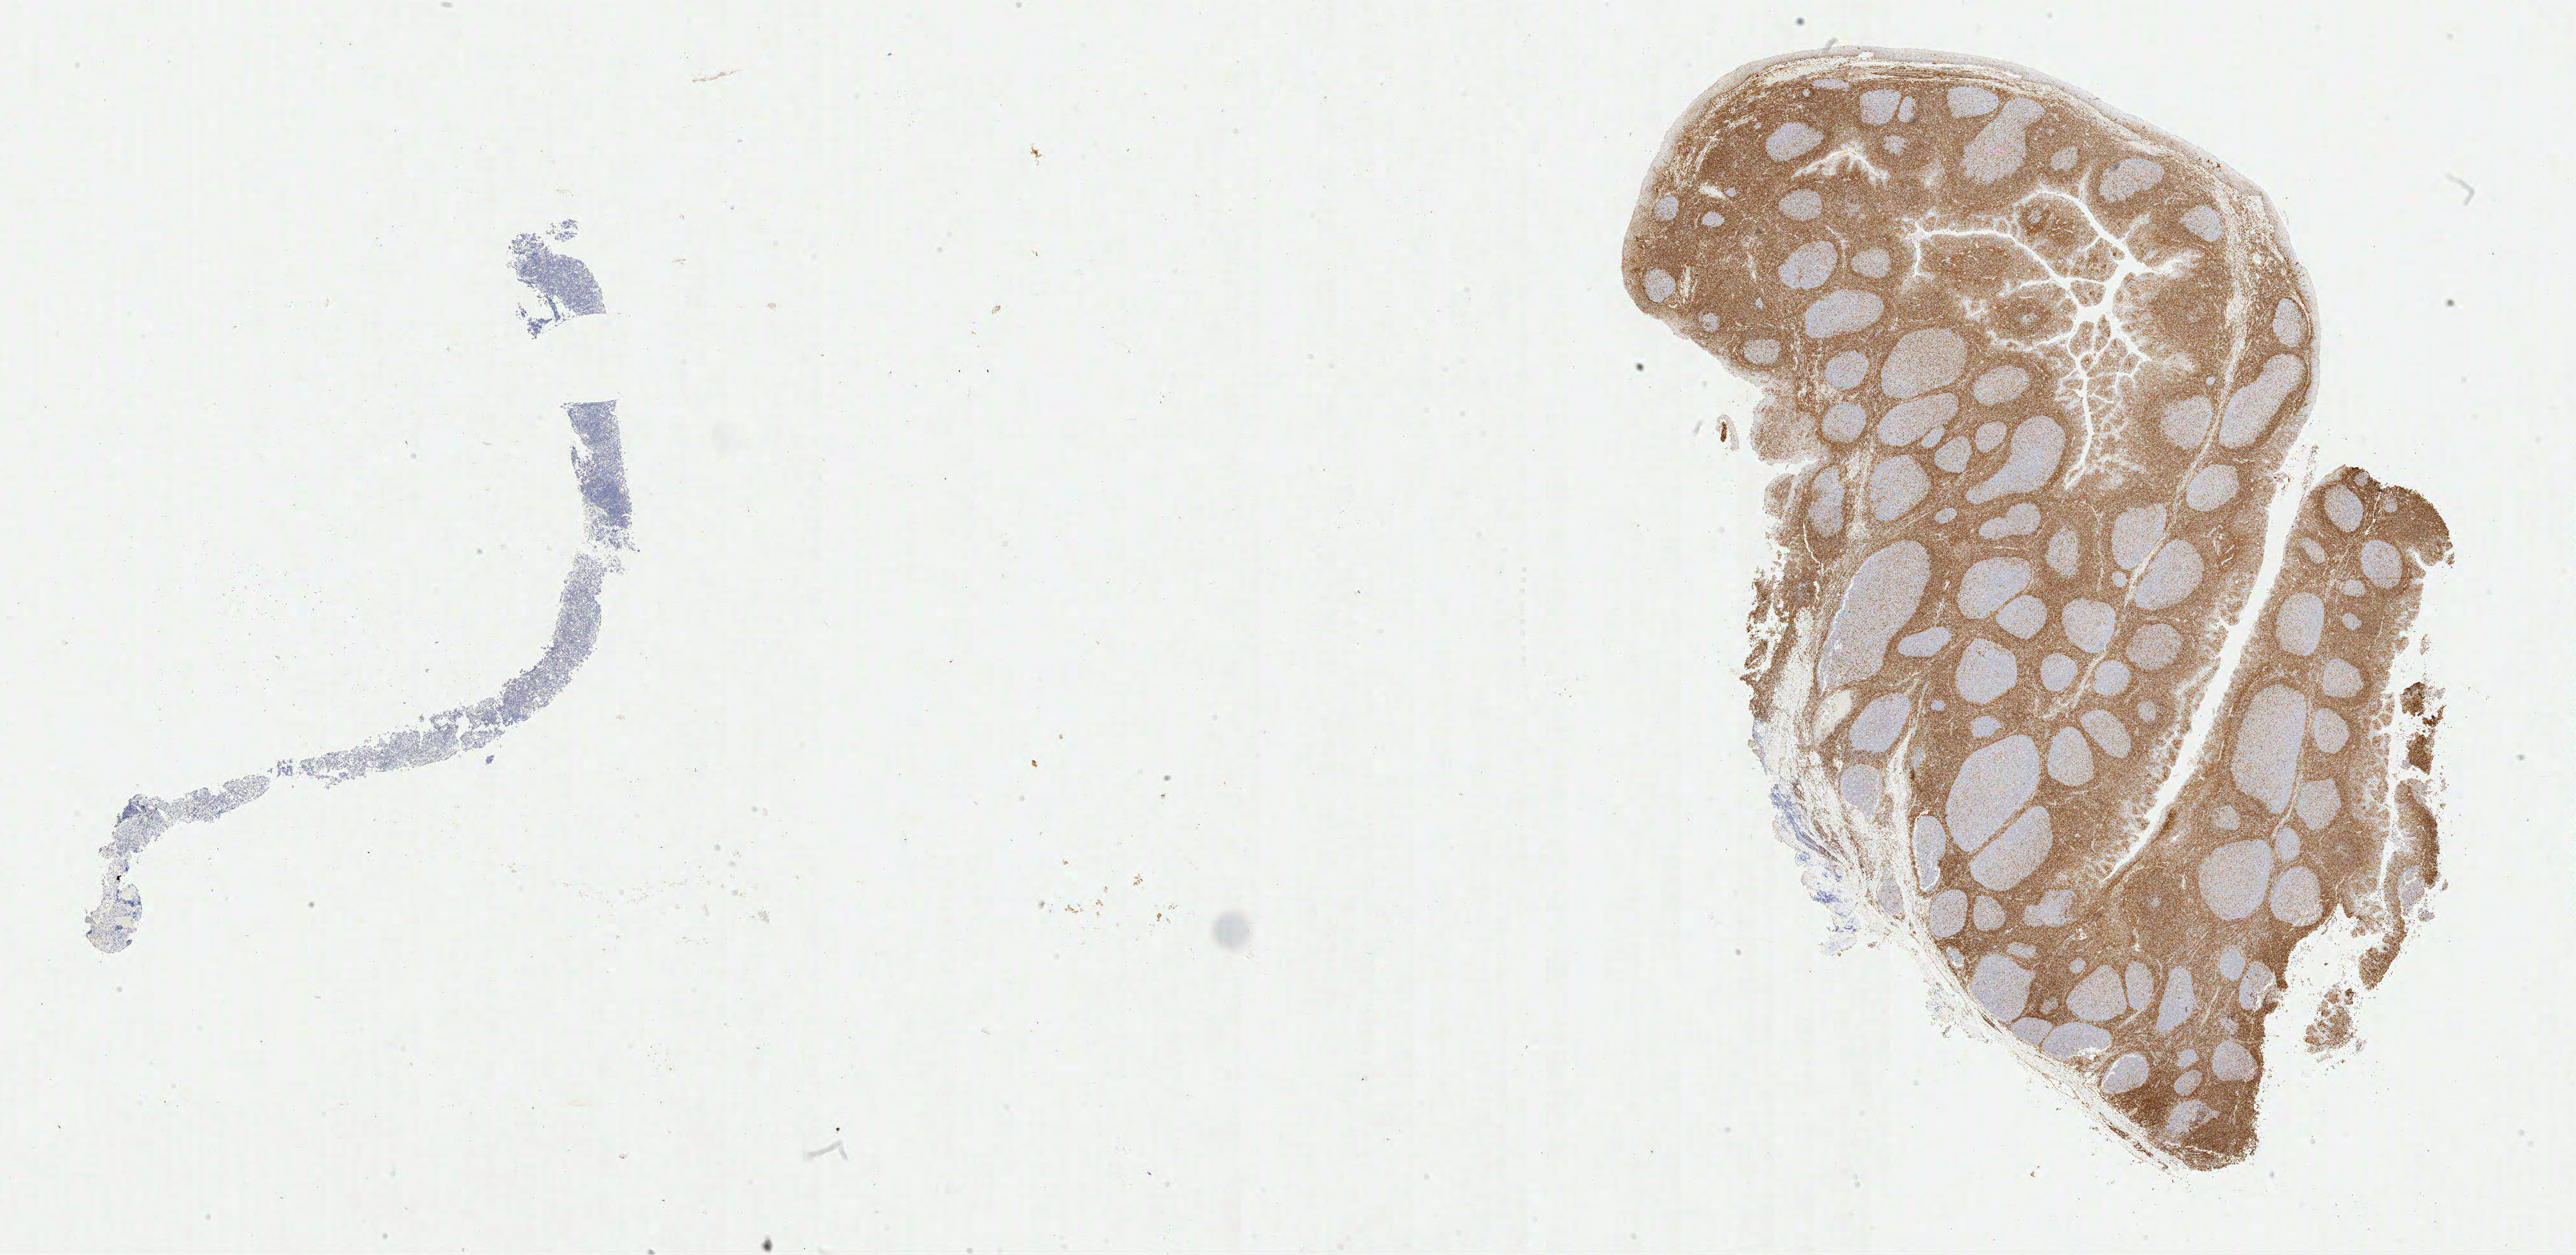
Whole-slide image, immunohistochemical stain for BCL2 — a low-resolution overview of the entire scanned area, about 31.7 x 15.4 mm, tumor tissue, anatomic site: ovary. Patient: female, age at initial diagnosis 7 years.
• diagnosis: Burkitt lymphoma, NOS